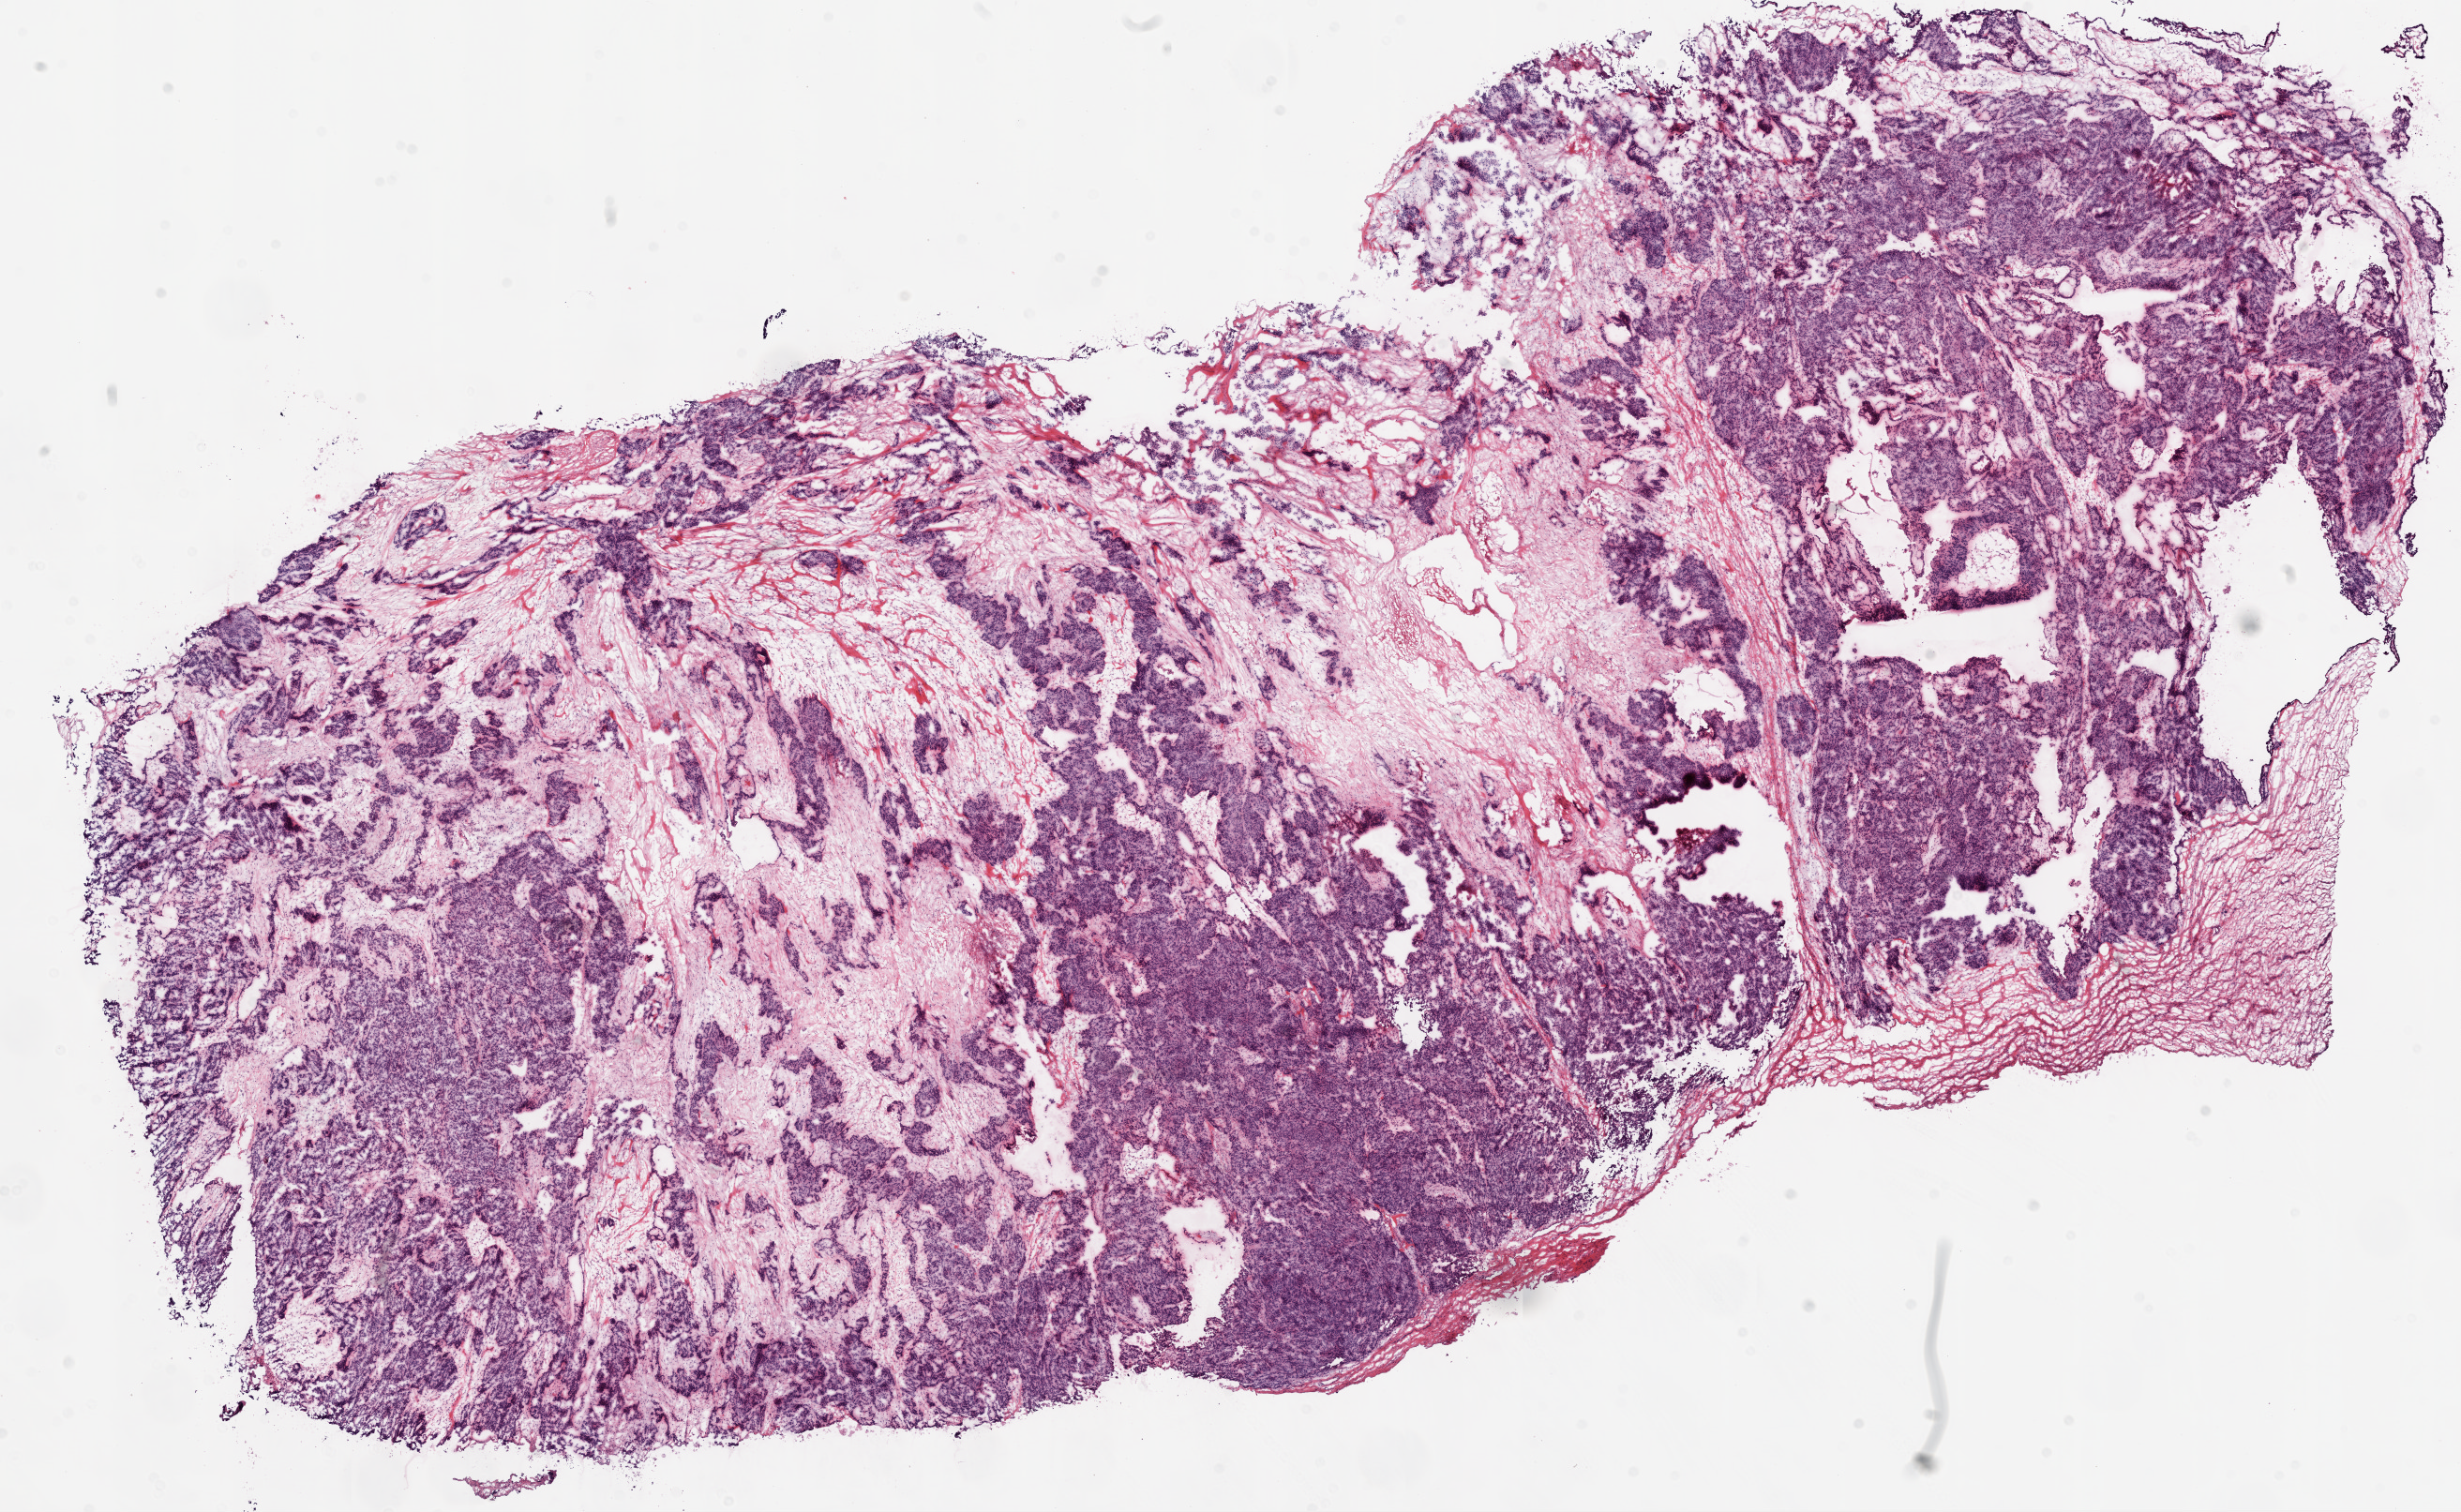
Whole-slide histology image, Hematoxylin and eosin (H&E) stained — a low-resolution overview of the entire scanned area, about 21.1 x 12.9 mm. Frozen section. Sample: primary tumour, ovary. Female, age 55 years at initial diagnosis. Histologic grade: G3 (poorly differentiated). Slide review estimates, as recorded: tumour cells 95%, tumour nuclei 95%, normal cells 0%, stromal cells 5%, necrosis 0%.
Laterality: bilateral. FIGO stage: IIIC. Diagnosis: Serous cystadenocarcinoma, NOS.